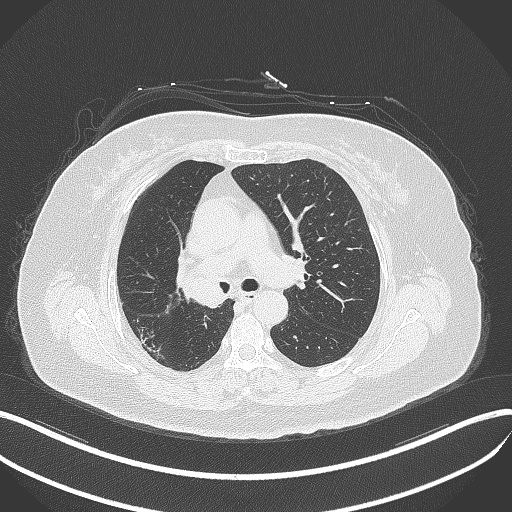
Chest CT, one axial slice; slice 226 of 376 in the series (ordered by position); reconstruction kernel B70f; 120 kVp; lung window (W 1500 / L -600 HU); 512 × 512 image matrix, field of view 400 × 400 mm. Patient: female, 60 years. From the clinical record (not read from this slice): clinical TNM (as recorded): T1c N0 M0.
Outlined on this slice (bounding box drawn by a radiologist):
- lung tumour (recorded histology: squamous cell carcinoma): bounding box (x1, y1, x2, y2) in pixels: (173, 264, 230, 311)